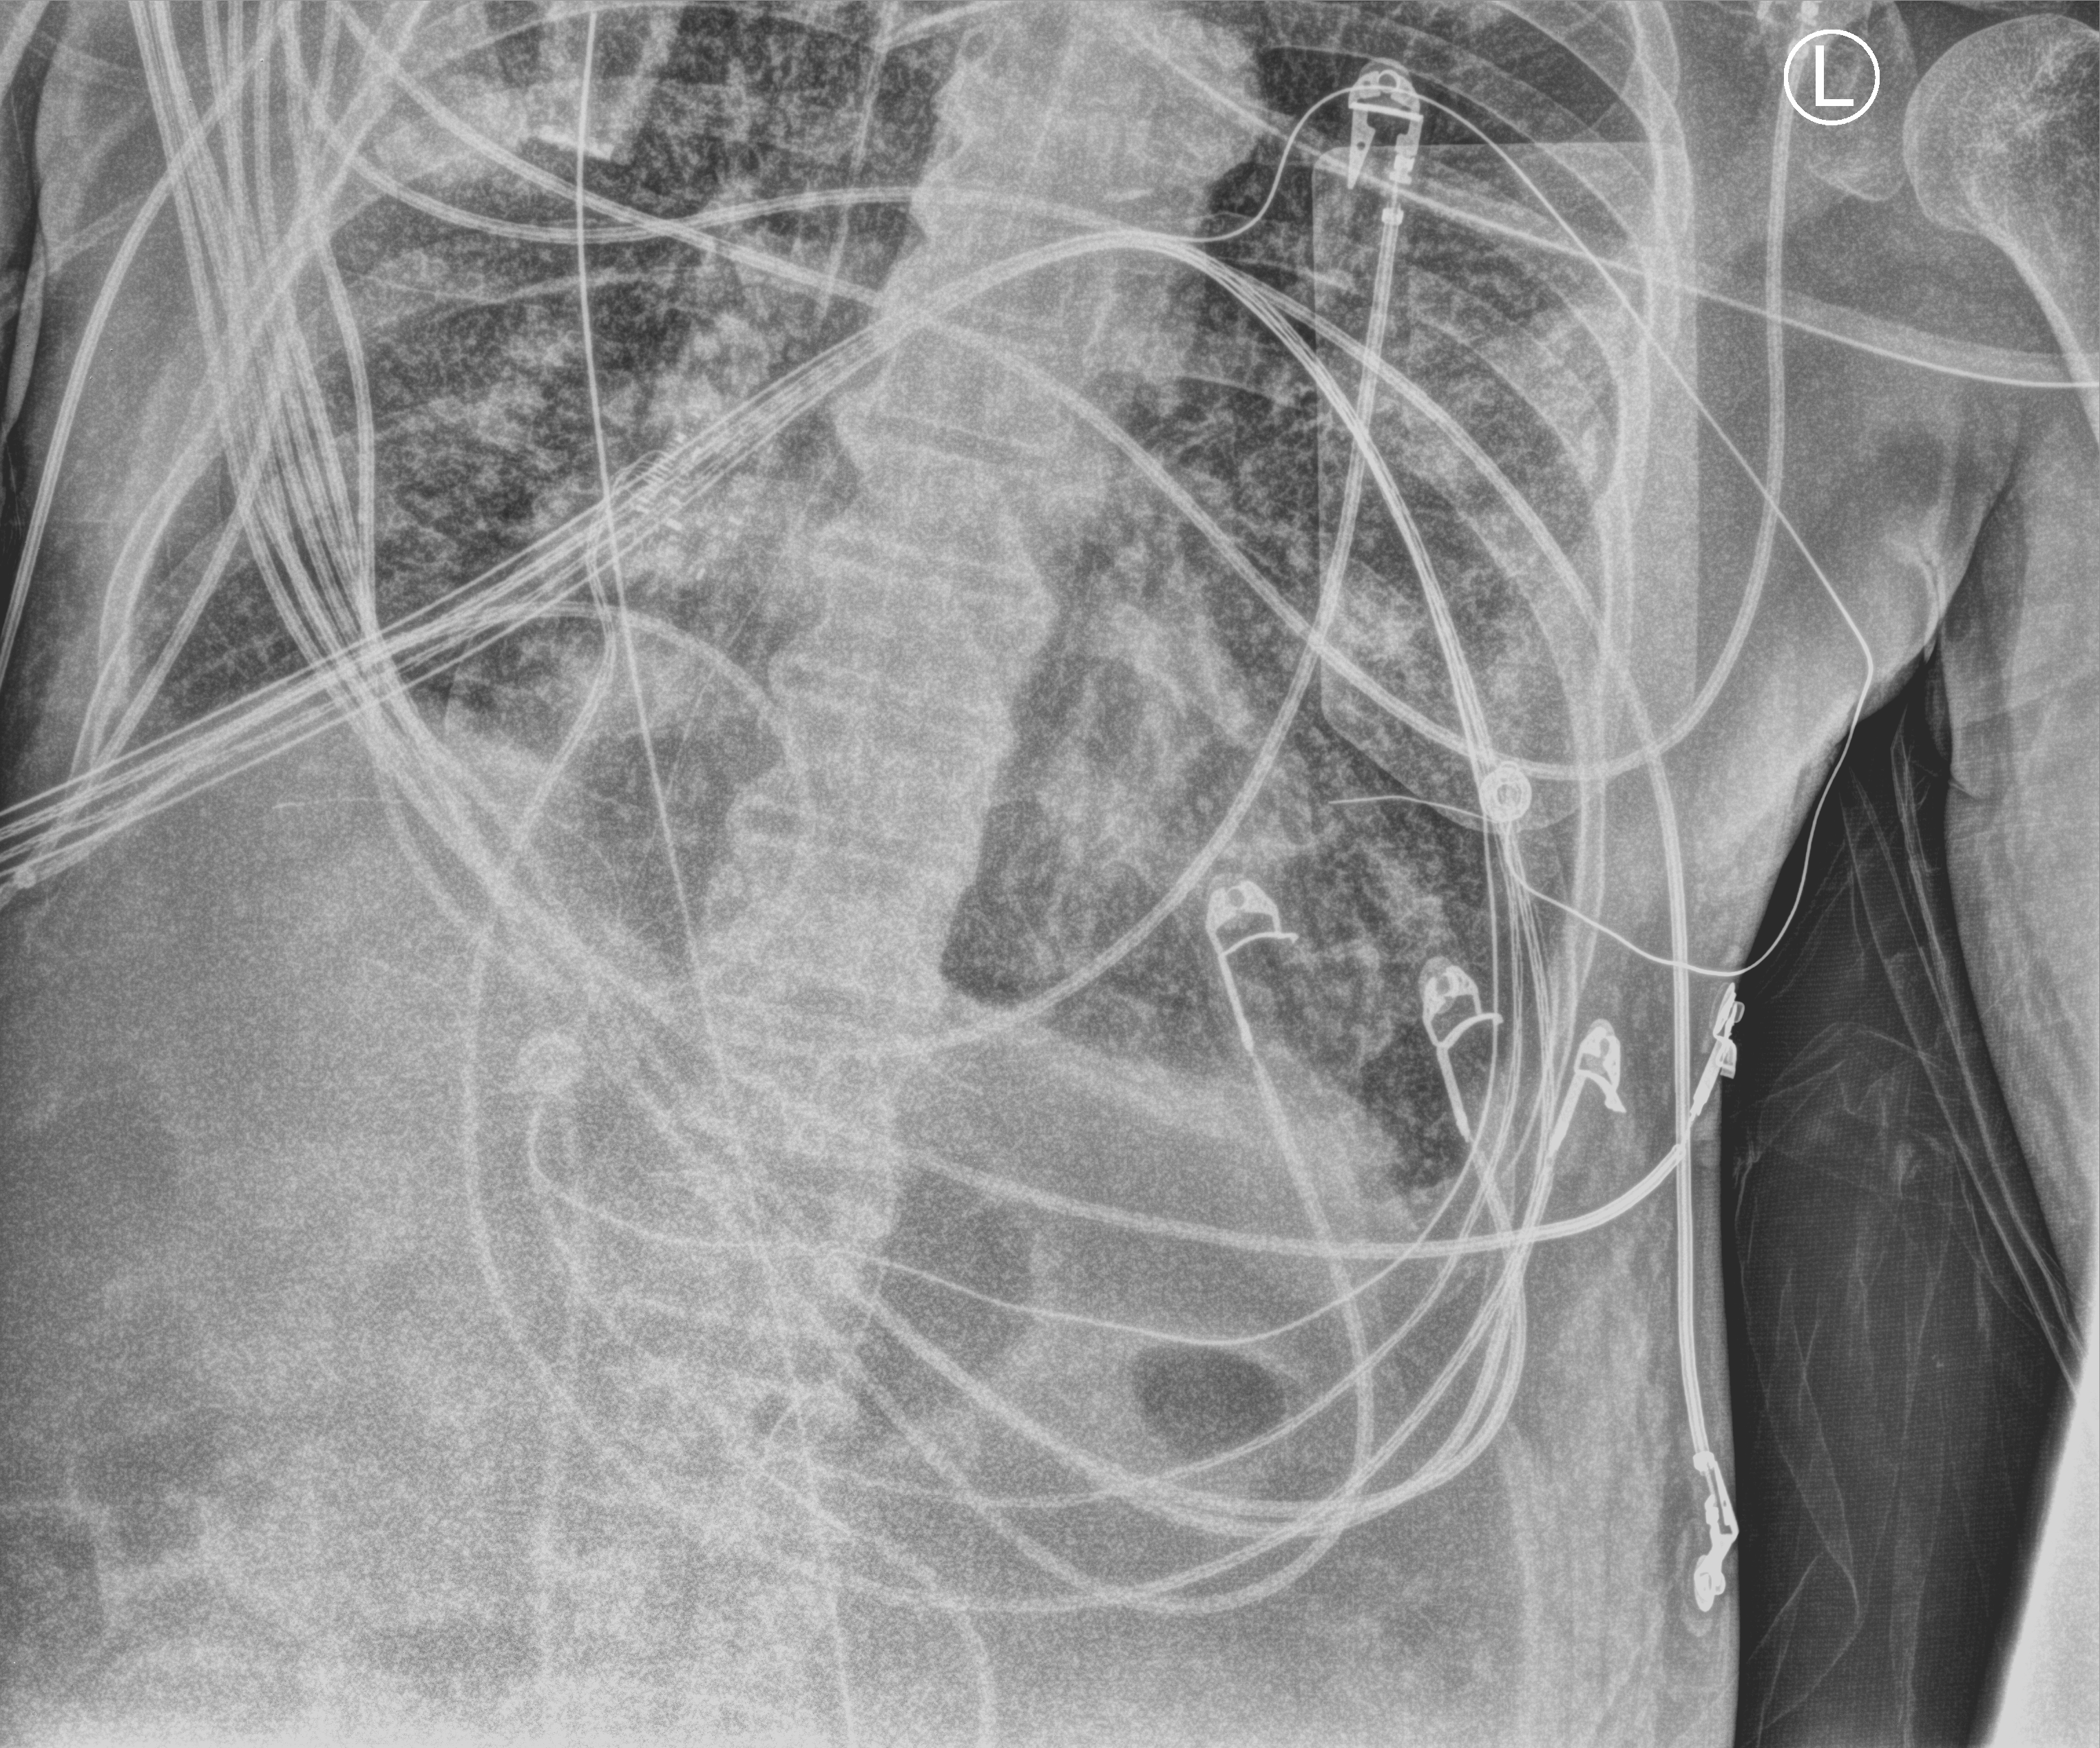
Portable chest radiograph. Male patient hospitalised with COVID-19, age 60–74 years.
Admission-level facts for this patient (not findings on this image; timing relative to this image not recorded): admitted to intensive care during this hospital stay: yes.